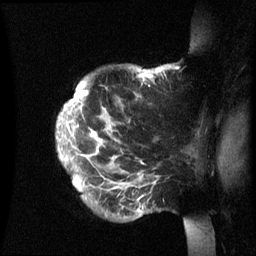
Breast MRI (dynamic contrast-enhanced), one sagittal slice. Position 51 of 60 along the scan axis. Dynamic contrast-enhanced series, image 2 of 3 at this slice position (ordered by acquisition). 1.5 T. TE 4.2 ms, TR 8.4 ms. 2.4 mm slice thickness. 256 × 256 image matrix, field of view 230 × 230 mm. Patient: female, 48 years.
Structures marked on this image (semi-automatically segmented with operator editing):
- analysis volume of interest (the breast-tissue region the enhancement analysis was run in; not a lesion): box from (x=57, y=65) to (x=200, y=236) px
- tumour enhancement mask (voxels above the 70 % enhancement threshold inside the analysis volume of interest): (x=58, y=67)–(x=163, y=211)